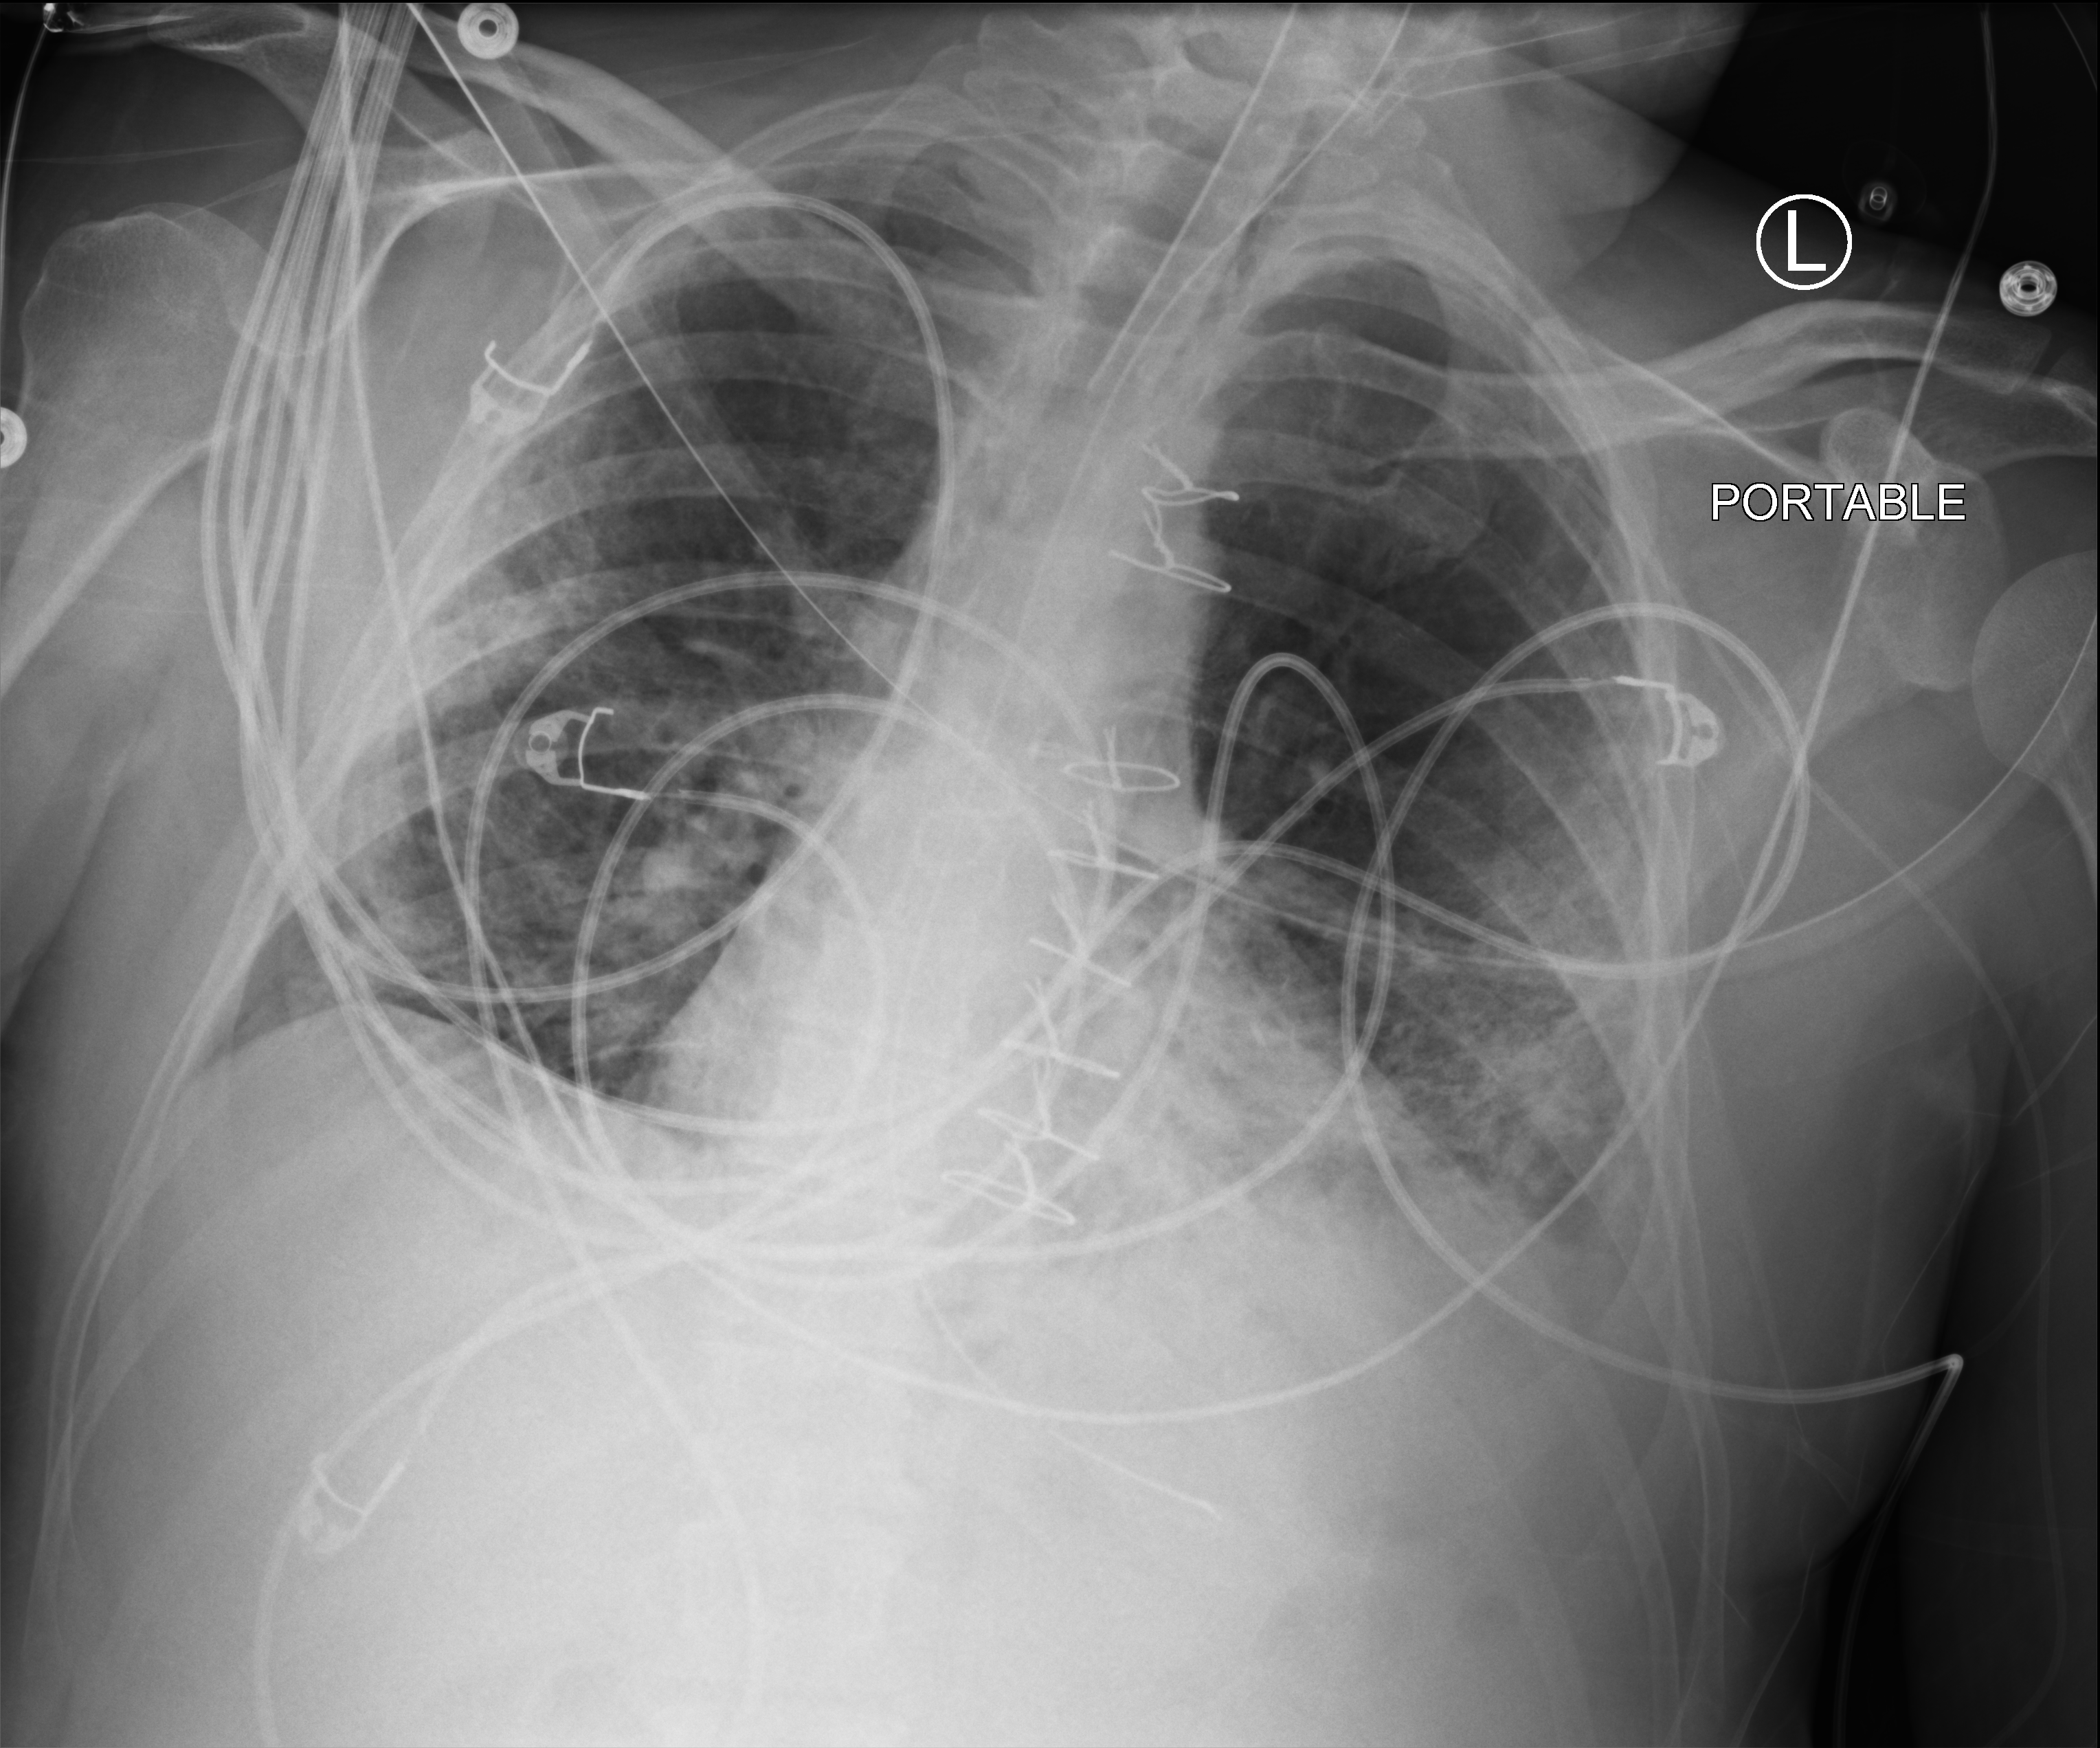
Portable chest radiograph, anteroposterior (AP) projection. Patient hospitalised with COVID-19; male, aged 18–59 years.
Admission-level facts for this patient (not findings on this image; timing relative to this image not recorded): admitted to intensive care during this hospital stay: yes.